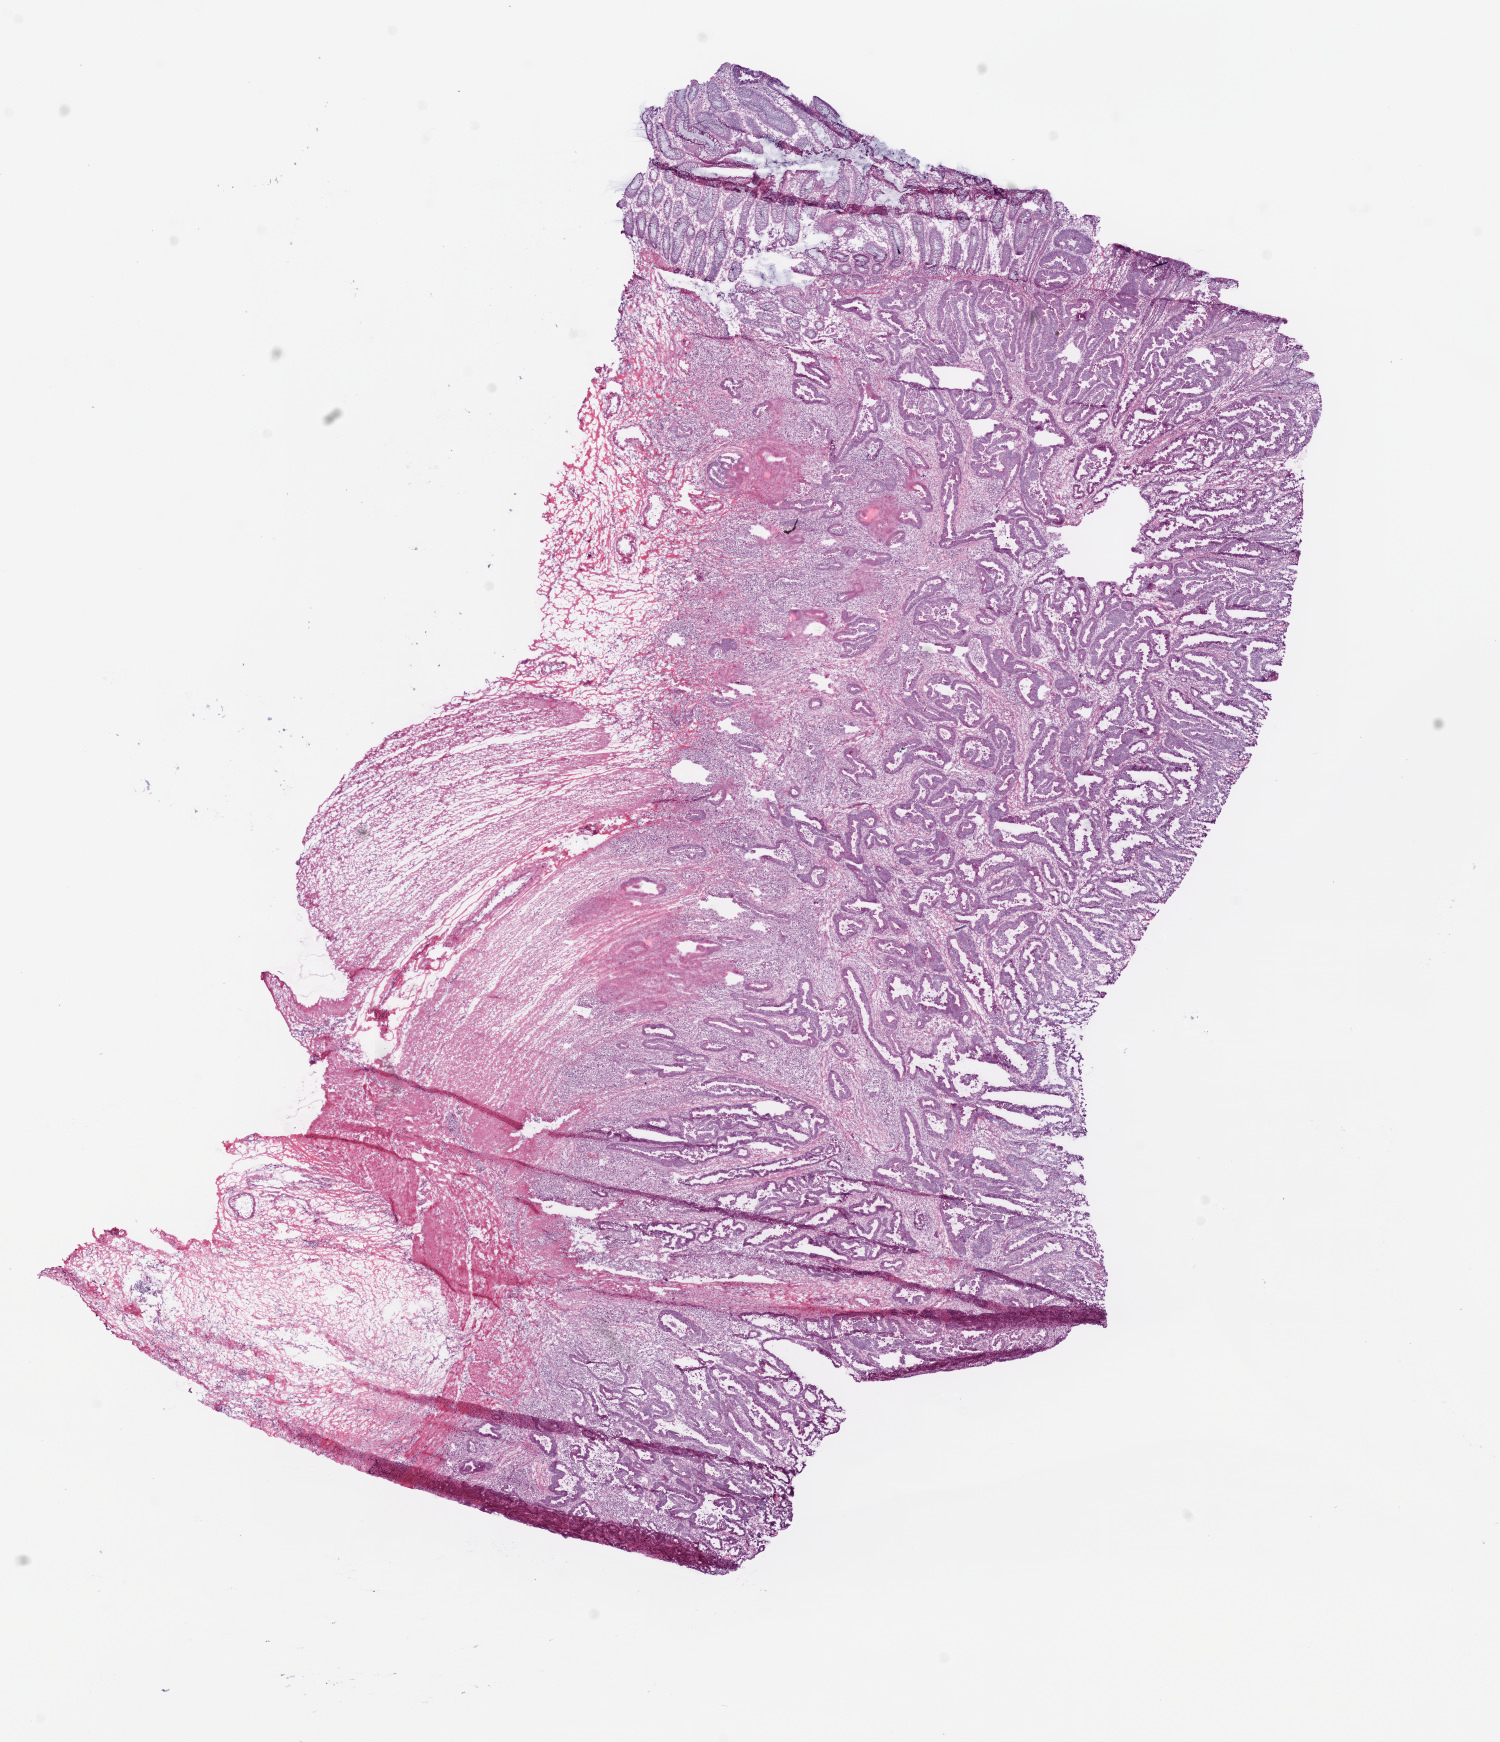
Digitized Hematoxylin and eosin (H&E) stained tissue section (whole slide) — shown as a low-resolution overview of the whole scanned area (about 12.0 x 14.0 mm), frozen section from the top of the tissue portion, sample: primary tumour, colon. Female, age 82 years at initial diagnosis. Pathologist review of this section (percent, as recorded): tumour nuclei 70%, normal cells 20%, stromal cells 10%, necrosis 5%.
Pathologic diagnosis: Adenocarcinoma, NOS (sigmoid colon). Lymph nodes positive (case pathology): 0 of 13 examined. AJCC pathologic stage: IIA.